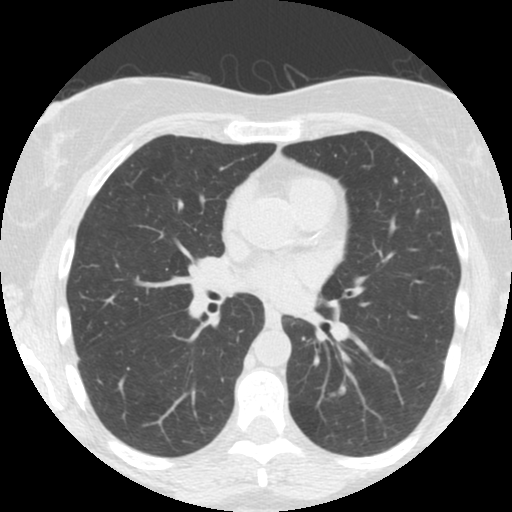
Low-dose screening chest CT, one axial slice. Slice 82 of 150 in the series (ordered by position). Reconstruction kernel STANDARD. 120 kVp. Lung window (W 1500 / L -600 HU). 2.5 mm slice thickness. 512 × 512 image matrix, field of view 300 × 300 mm.
Outlined on this slice (expert manual segmentation):
- lesion 1 (tumor, lower lobe of left lung): bounding box [x1, y1, x2, y2] px = [339, 385, 346, 394]